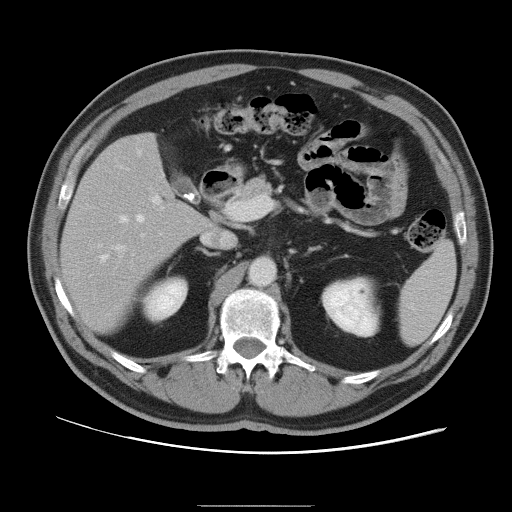
Contrast-enhanced abdominal CT, one axial slice; position 54 of 105 along the scan axis; intravenous contrast given; soft-tissue window (W 400 / L 40 HU); 512 × 512 image matrix. Male patient, age 64 years. Case-level facts recorded for this patient, not image findings: diagnosis: colorectal cancer liver metastases, imaged before liver resection; multiple liver metastases: yes; largest metastasis: 3 cm; disease in both lobes: yes.
Outlined on this slice (manually delineated by an expert):
- hepatic veins: bounding box (x1, y1, x2, y2) in pixels: (101, 169, 144, 261)
- liver: (63, 134, 211, 332)
- planned liver remnant (the part of the liver to remain after resection): (63, 134, 211, 332)
- portal vein (with intrahepatic branches): (113, 194, 164, 251)